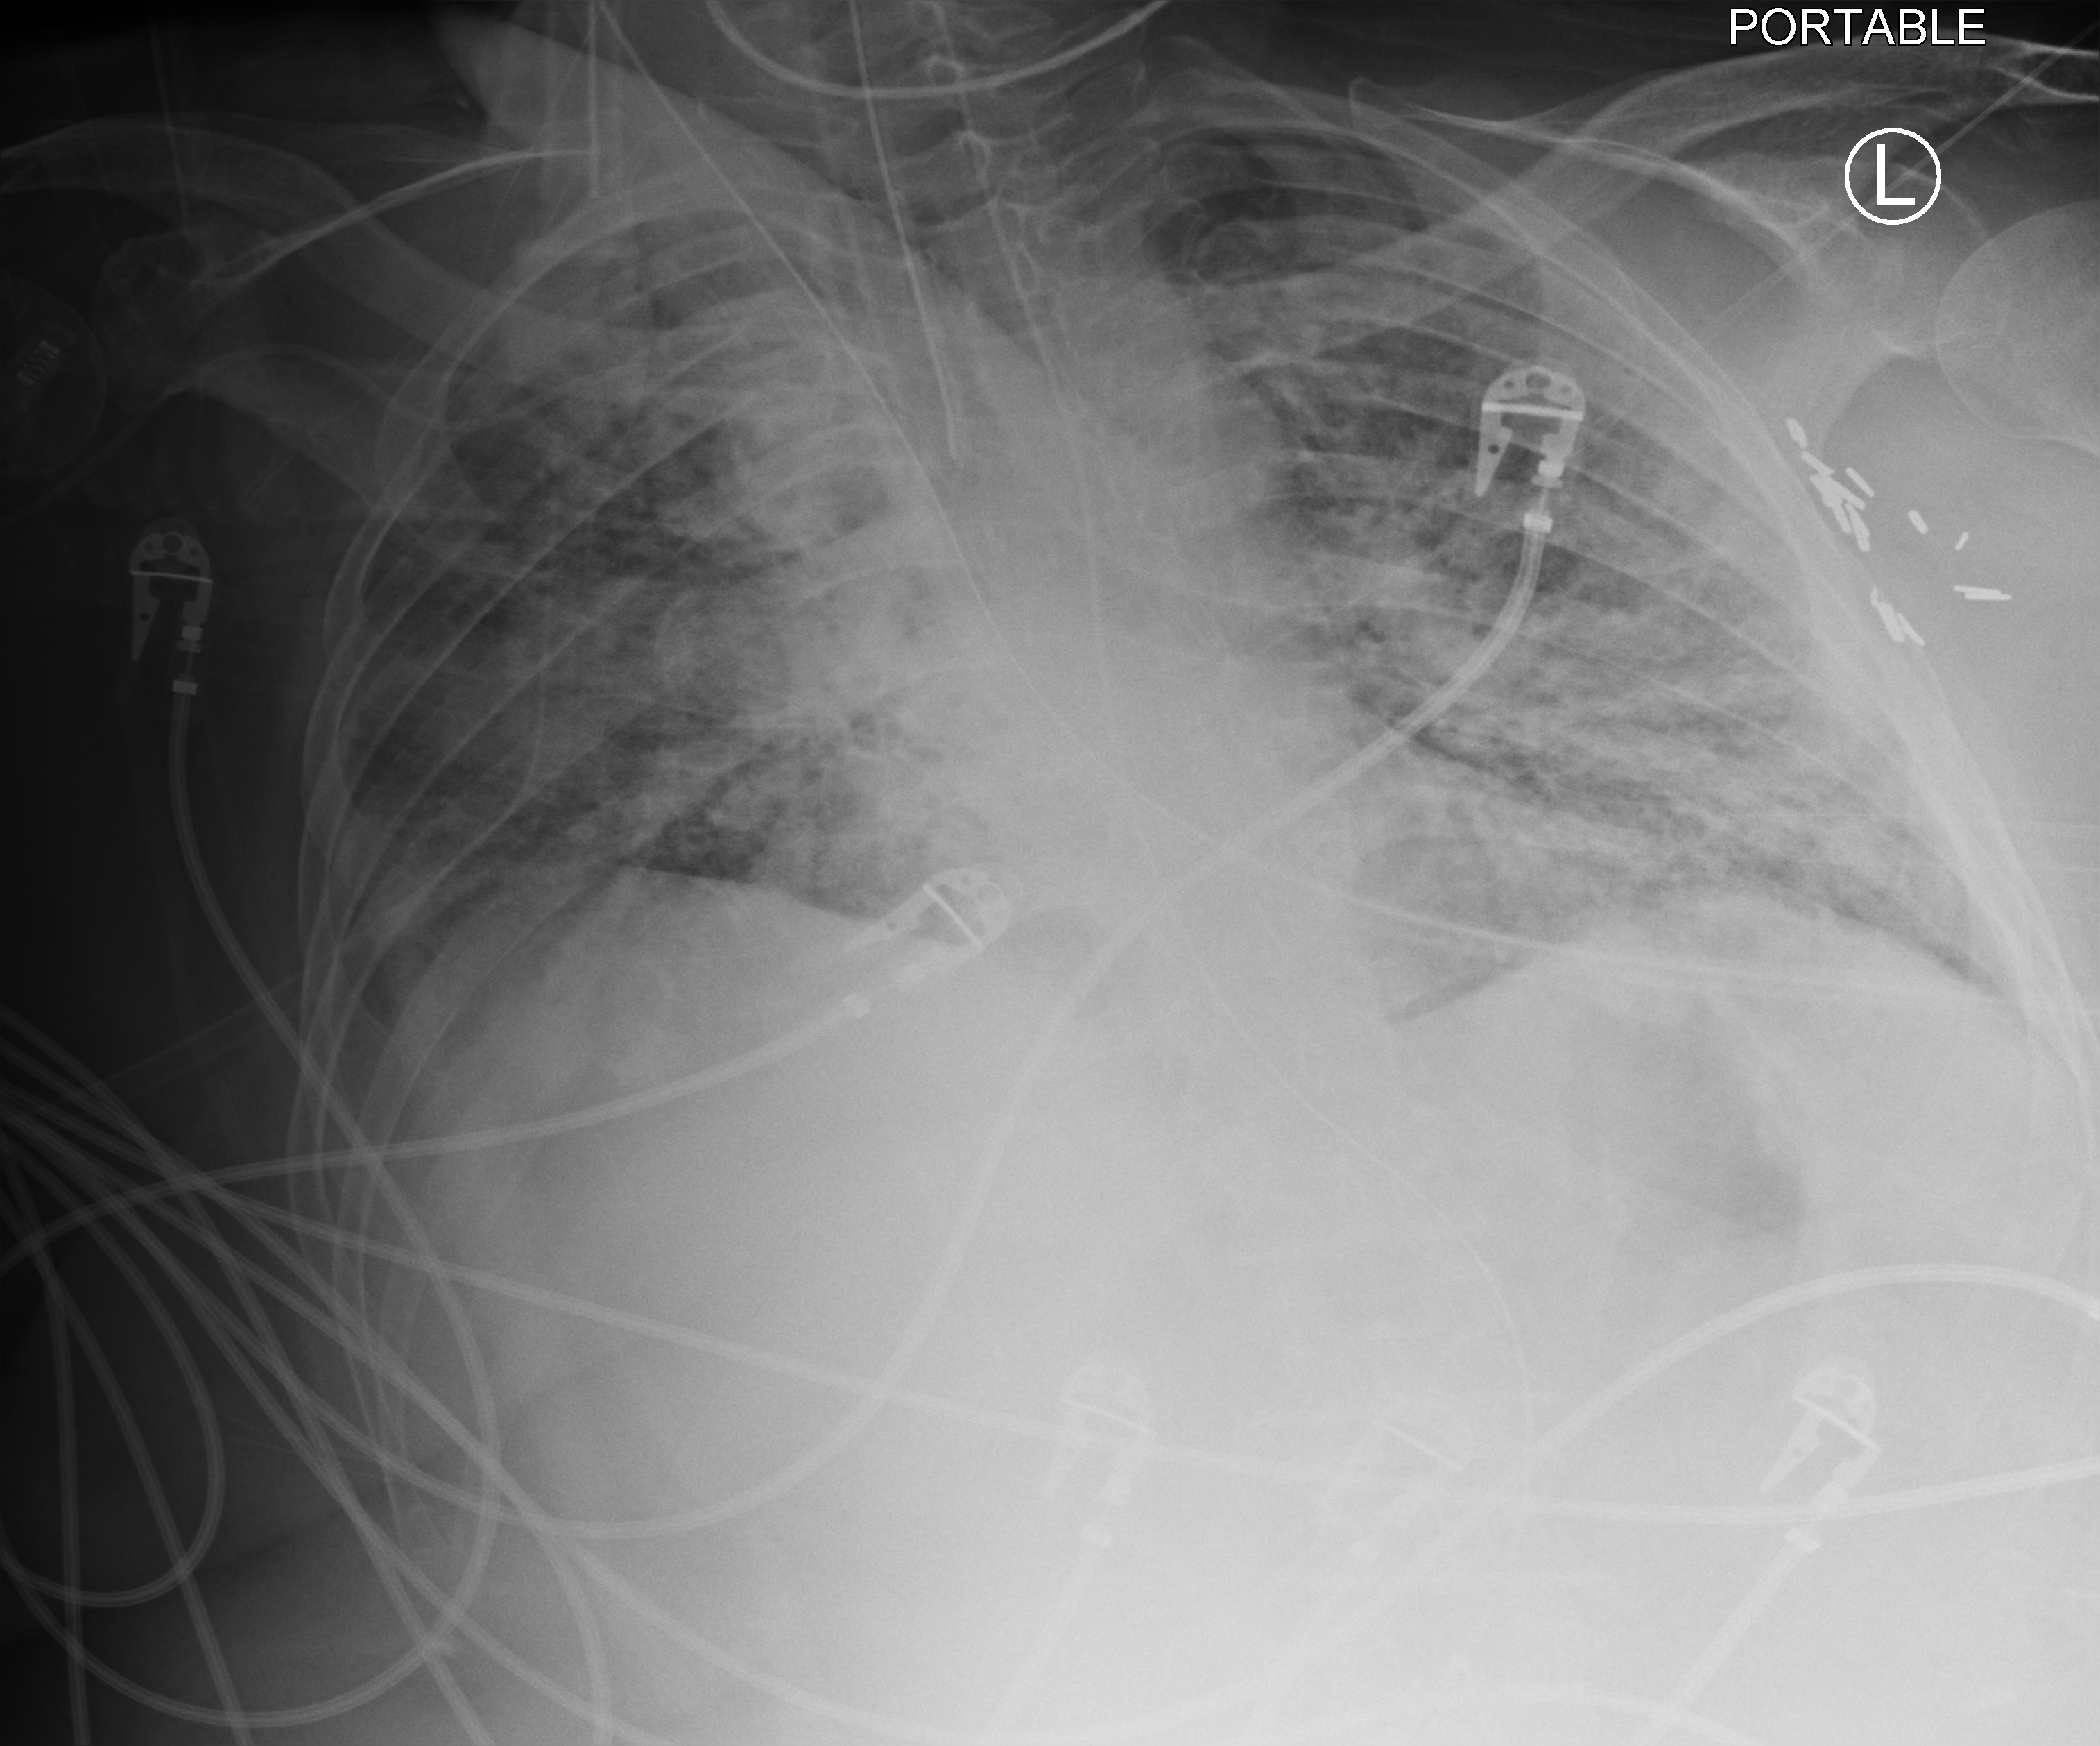
Portable chest radiograph; anteroposterior (AP) projection. Patient hospitalised with COVID-19; female, aged 60–74 years.
From the hospital-stay record, not from the radiograph (when in the stay this image was taken is not recorded): hypertension (admission record): yes; admitted to intensive care during this hospital stay: yes.